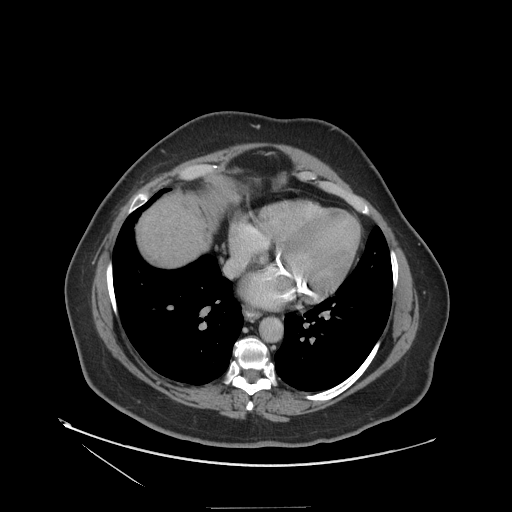
Contrast-enhanced abdominal CT (liver protocol), one axial slice; position 109 of 127 along the scan axis; soft-tissue window (W 400 / L 40 HU); 2.5 mm slice thickness; 512 × 512 image matrix, field of view 480 × 480 mm. From the clinical record (not read from this slice): diagnosis: hepatocellular carcinoma (patient treated with transarterial chemoembolisation; whether this scan precedes or follows treatment is not stated here); TNM stage (as recorded): Stage-II; Child-Pugh class: A; tumour differentiation: well differentiated; tumour nodularity: multinodular.
Structures marked on this image (semi-automatically segmented with operator editing):
- liver parenchyma outside the tumour (the mass and vessels are separate outlines, so this box may not span the whole liver): bounding box (x1, y1, x2, y2) in pixels: (136, 194, 210, 266)